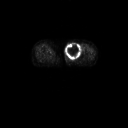
FDG PET of an extremity soft-tissue mass (from a PET/CT study), one axial slice; slice 32 of 91 in the series (ordered by position); 3.27 mm slice thickness; 128 × 128 image matrix, field of view 700 × 700 mm. Female patient, age 74 years. Case-level facts recorded for this patient, not image findings: histological type: pleomorphic leiomyosarcoma; grade: high; site of the primary tumour: left thigh.
Outlined on this slice (expert contour drawn on MRI and transferred to this co-registered scan by the dataset authors):
- gross tumour volume including surrounding oedema: bounding box <65,41,82,60> (left, top, right, bottom; pixels)
- gross tumour volume (mass): <65,42,82,59>